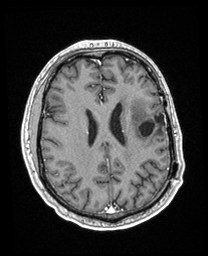
Brain MRI from a brain-tumour surgery series, one axial slice; slice 85 of 208 in the series (ordered by position); T1-weighted post-contrast; 1 mm slice thickness; 208 × 256 image matrix. Case-level facts recorded for this patient, not image findings: histopathology: Astrocytoma; WHO grade: 3; IDH mutation: yes.
Outlined on this slice (expert manual segmentation):
- previous resection cavity: bounding box <139,113,165,136> (left, top, right, bottom; pixels)